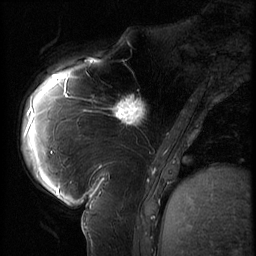
Breast MRI (dynamic contrast-enhanced), one sagittal slice; position 20 of 62 along the scan axis; 3 images stored at this slice position (order not interpretable as contrast timing); 1.5 T; TE 4.2 ms, TR 9 ms; 2.5 mm slice thickness; 256 × 256 image matrix, field of view 180 × 180 mm. Patient: female, 57 years. From the clinical record (not read from this slice): setting: breast cancer imaged before/during neoadjuvant chemotherapy; receptor status: triple-negative.
Outlined on this slice (semi-automatically segmented with operator editing):
- analysis volume of interest (the breast-tissue region the enhancement analysis was run in; not a lesion): bounding box <105,84,158,135> (left, top, right, bottom; pixels)
- tumour enhancement mask (voxels above the 140 % enhancement threshold inside the analysis volume of interest): <112,94,147,125>